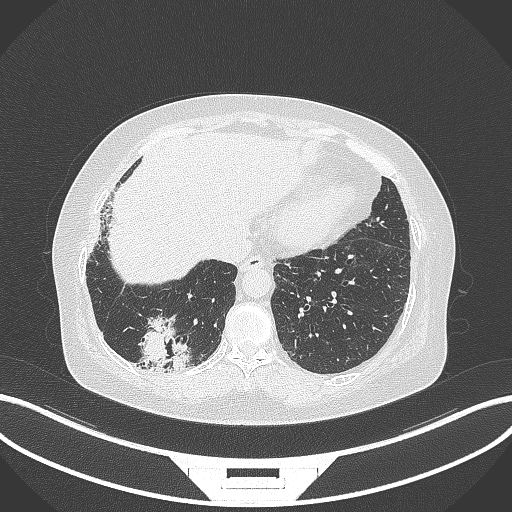
Chest CT, one axial slice. Slice 42 of 296 in the series (ordered by position). Reconstruction kernel B70f. 120 kVp. Lung window (W 1500 / L -600 HU). 512 × 512 image matrix. Patient: female, 65 years. Case-level facts recorded for this patient, not image findings: clinical TNM (as recorded): T2b N1 M0.
Structures marked on this image (rectangle marked by the reading radiologist):
- lung tumour (recorded histology: adenocarcinoma): bounding box <135,311,191,371> (left, top, right, bottom; pixels)